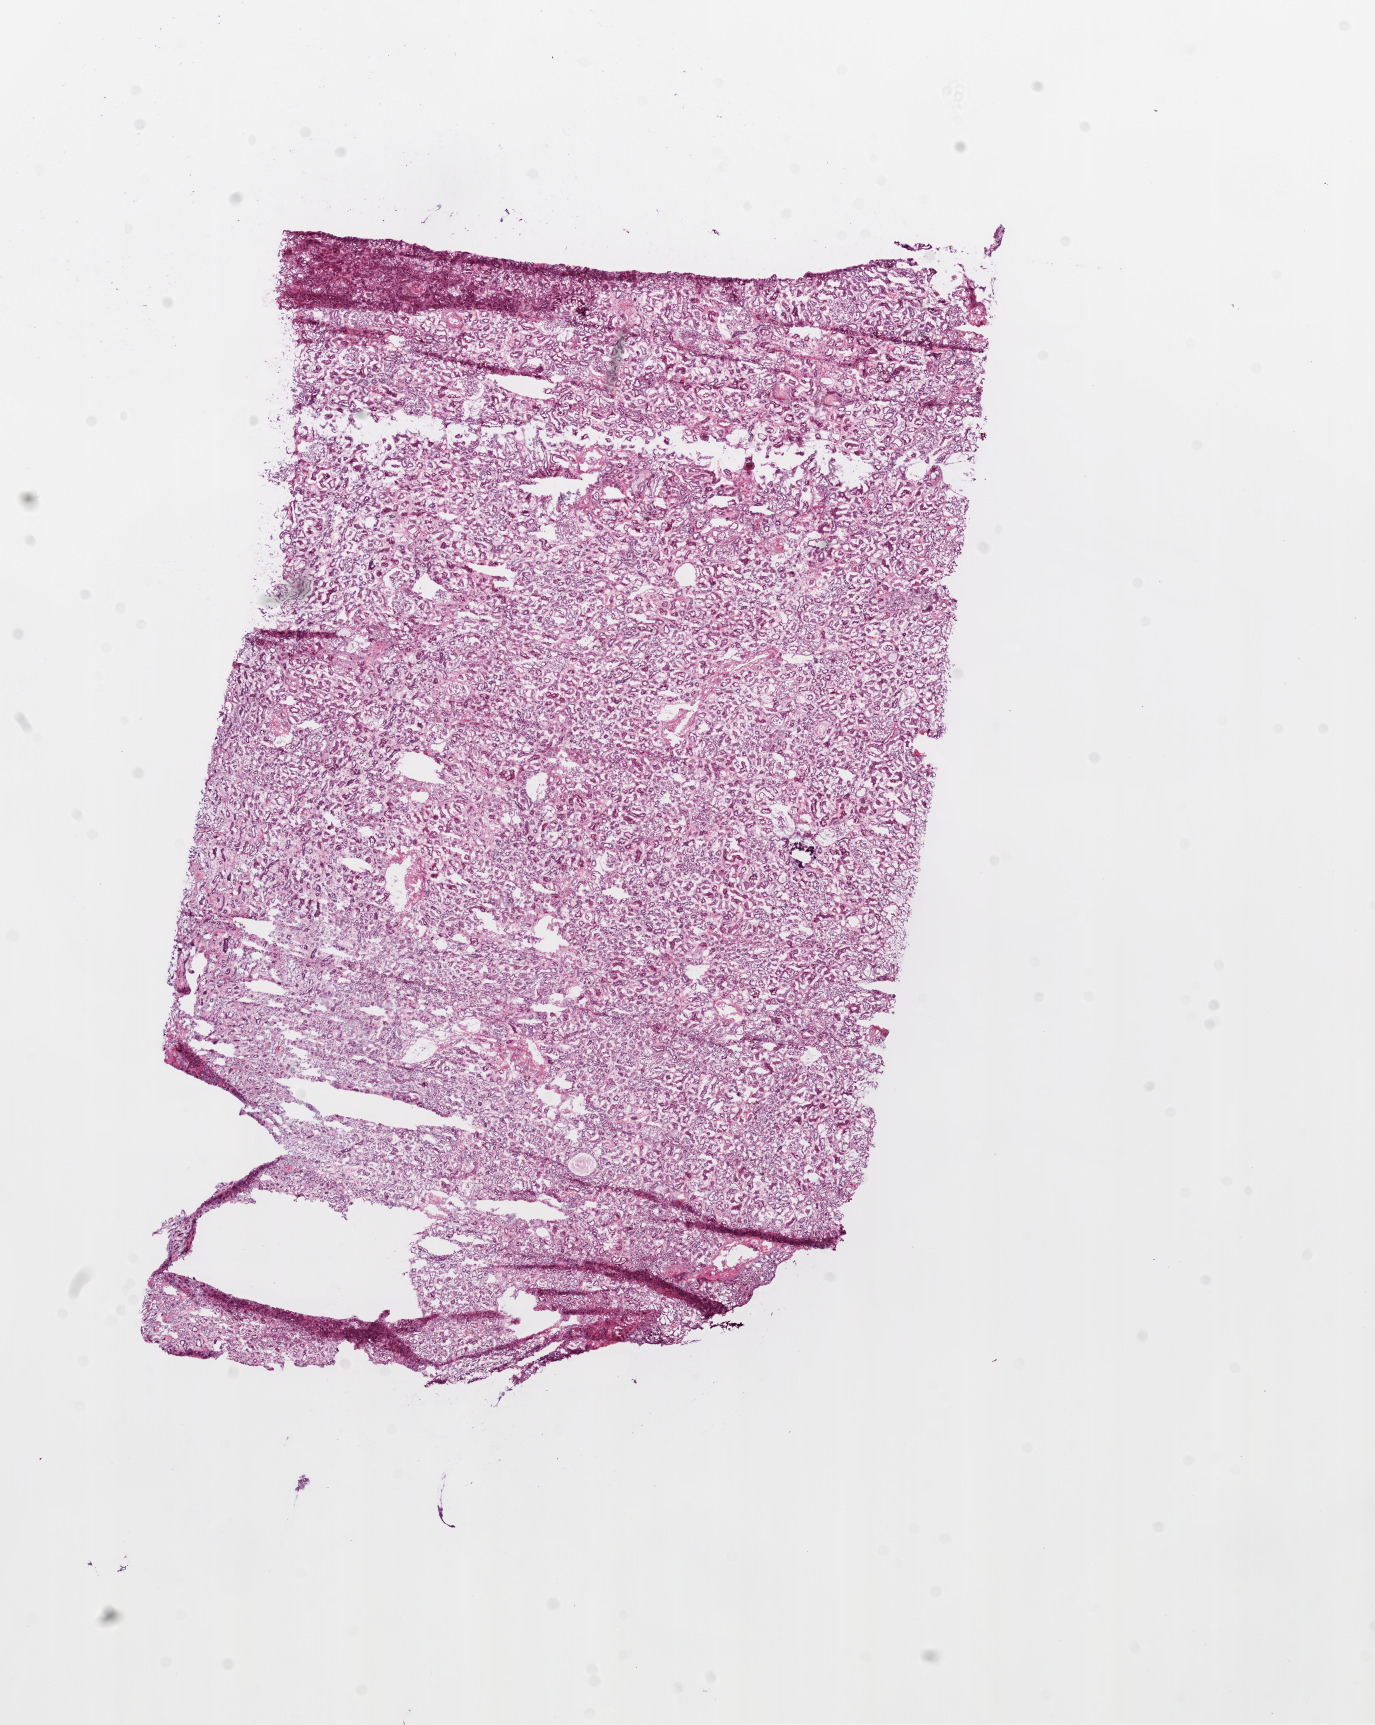
Digitized H&E-stained tissue section (whole slide) — whole scanned area (about 11.0 x 13.8 mm, from a 20x scan) shown as a low-resolution overview, frozen section from the top of the tissue portion, sample: solid tissue normal (non-tumour tissue), kidney. Male, age 66 years at initial diagnosis.
This section: solid tissue normal sample (biorepository sample class). Patient diagnosis: Clear cell adenocarcinoma, NOS.